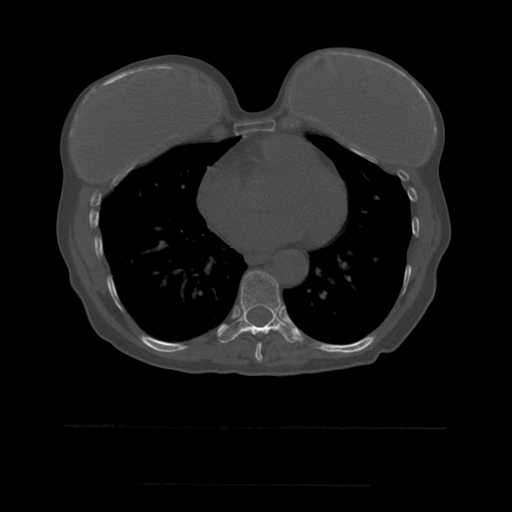
CT including the spine, one axial slice; position 326 of 544 along the scan axis; bone window (W 1800 / L 400 HU); 1.25 mm slice thickness; 512 × 512 image matrix. Patient age 58 years. Case-level facts recorded for this patient, not image findings: primary cancer: lung.
Structures marked on this image (semi-automatically segmented with operator editing):
- T8 vertebra: box from (x=255, y=343) to (x=263, y=361) px
- T9 vertebra: (x=217, y=271)–(x=302, y=343)